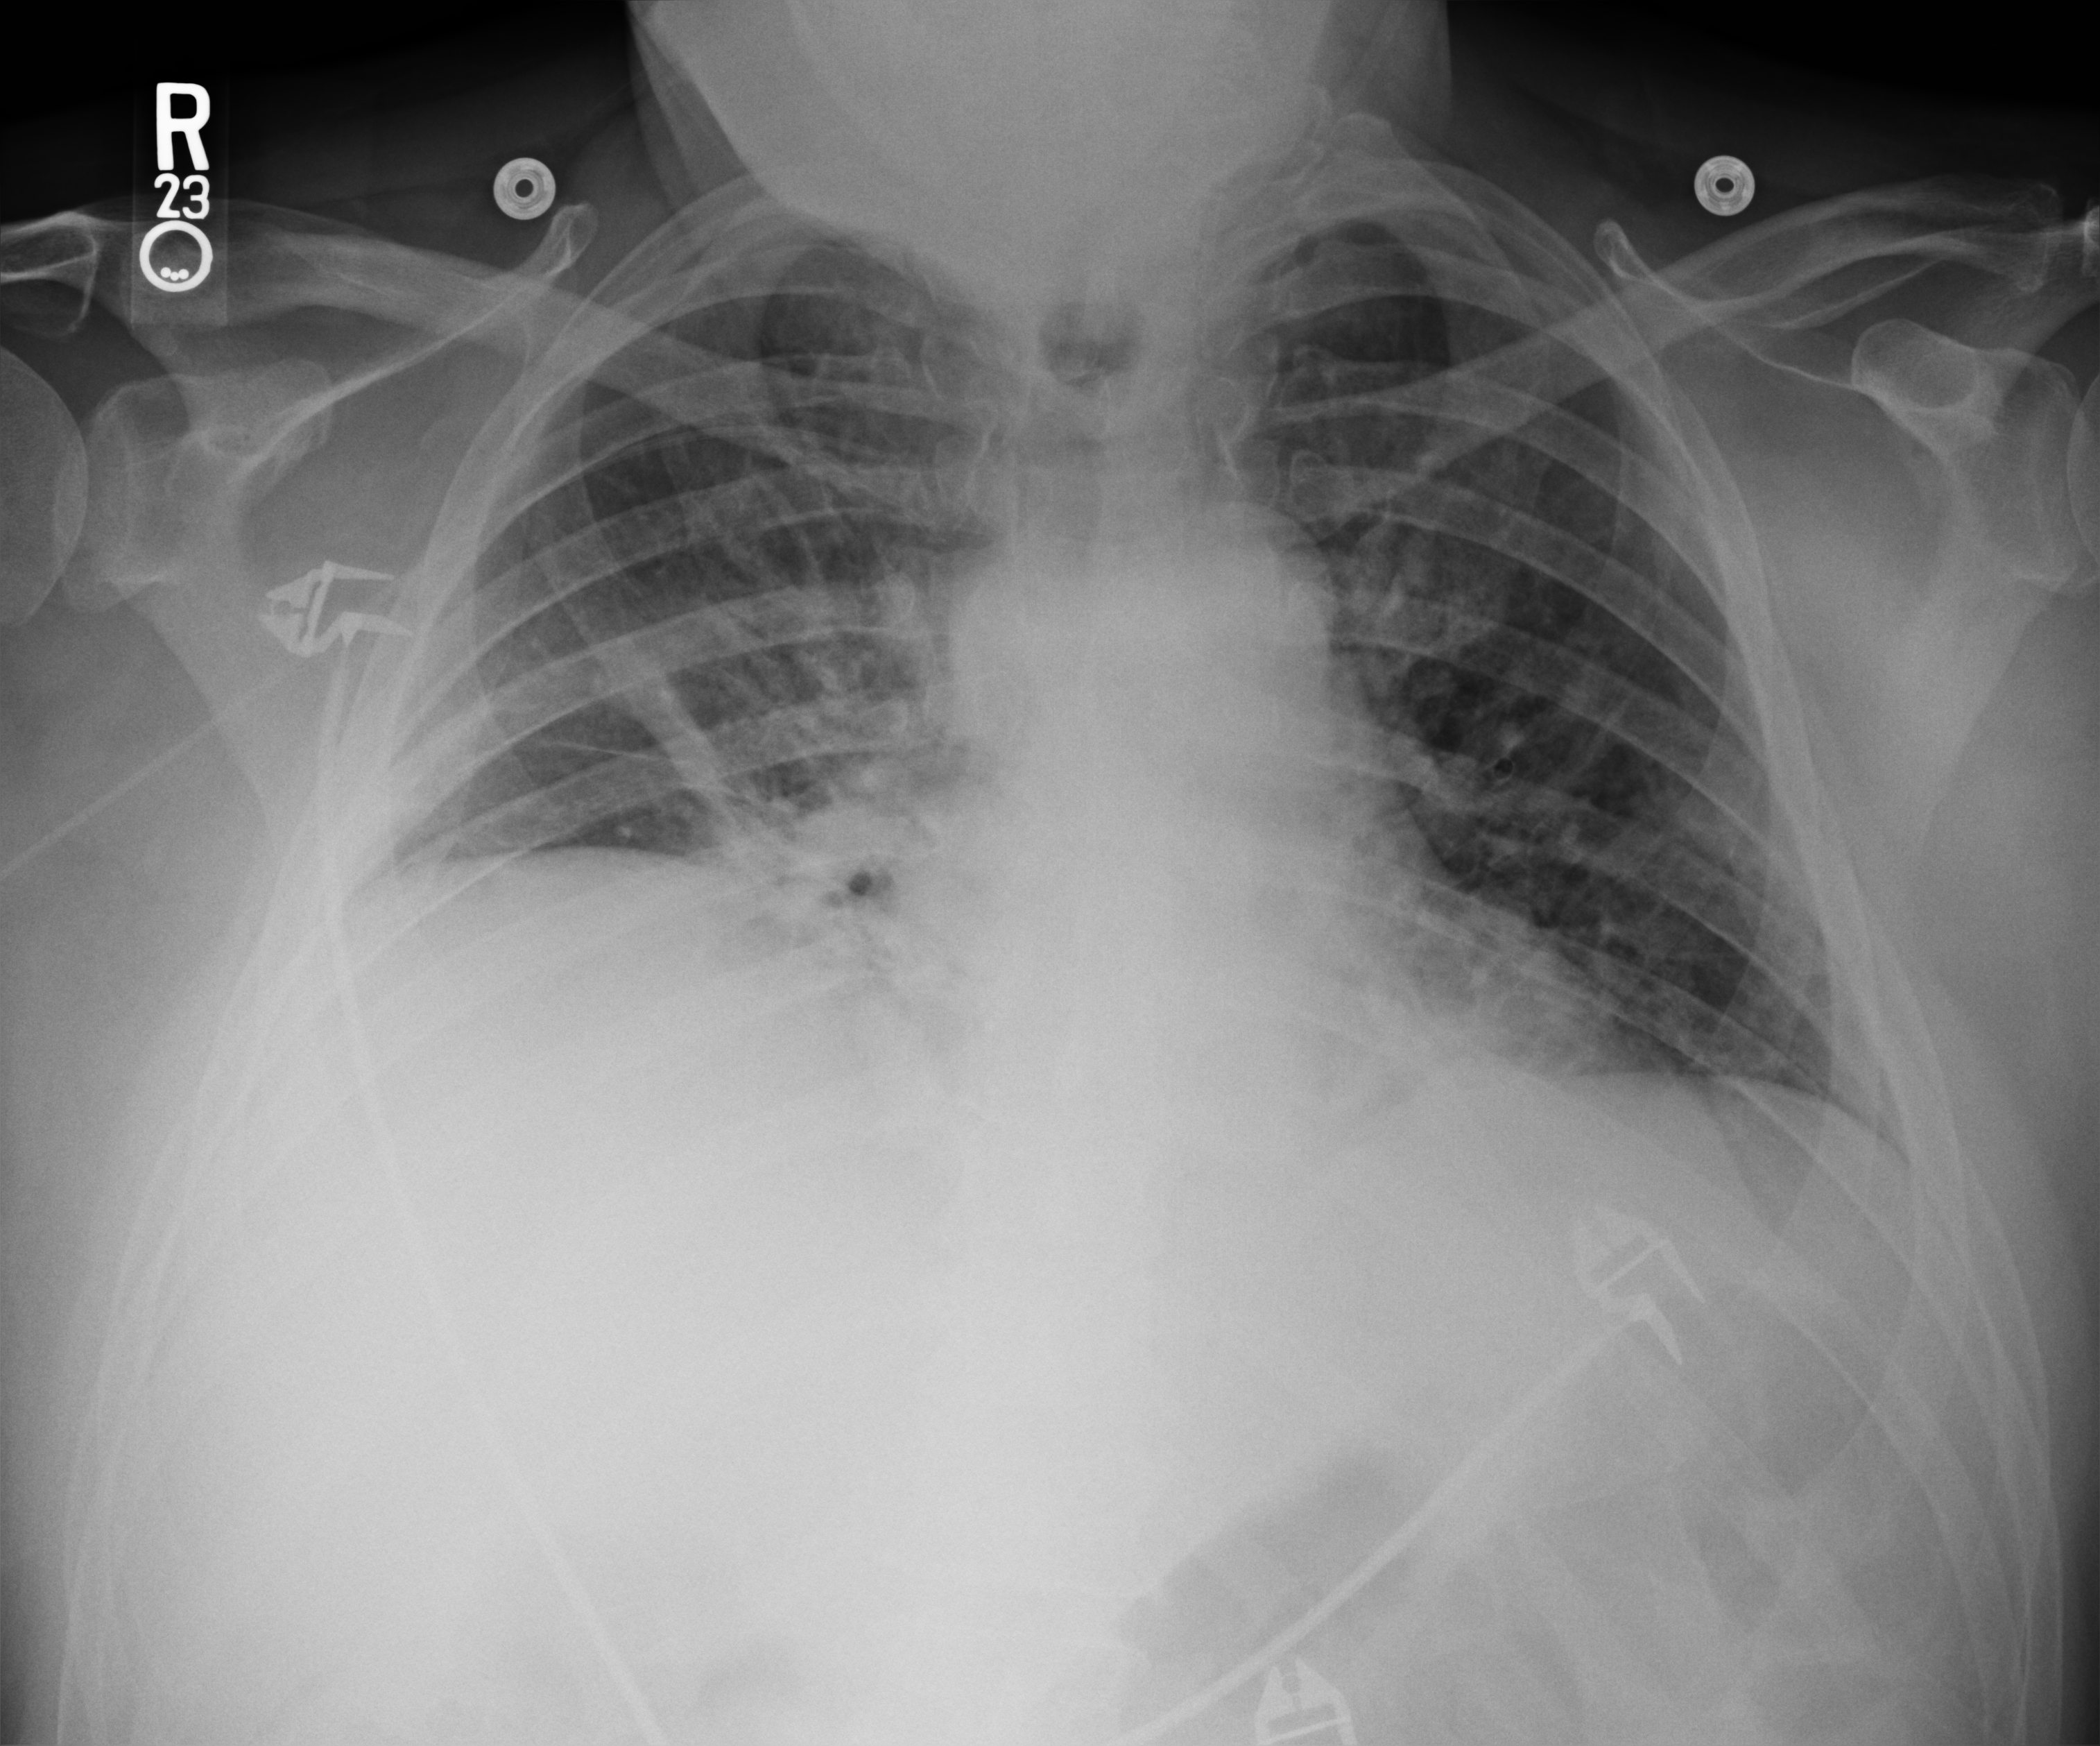
Chest X-ray (portable), anteroposterior (AP) projection. Patient hospitalised with COVID-19; male, aged 18–59 years.
Hospital-stay facts (about this admission, not read from this image; timing relative to this image not recorded): mechanically ventilated during this hospital stay: yes; admitted to intensive care during this hospital stay: yes; smoking status (admission record): never.